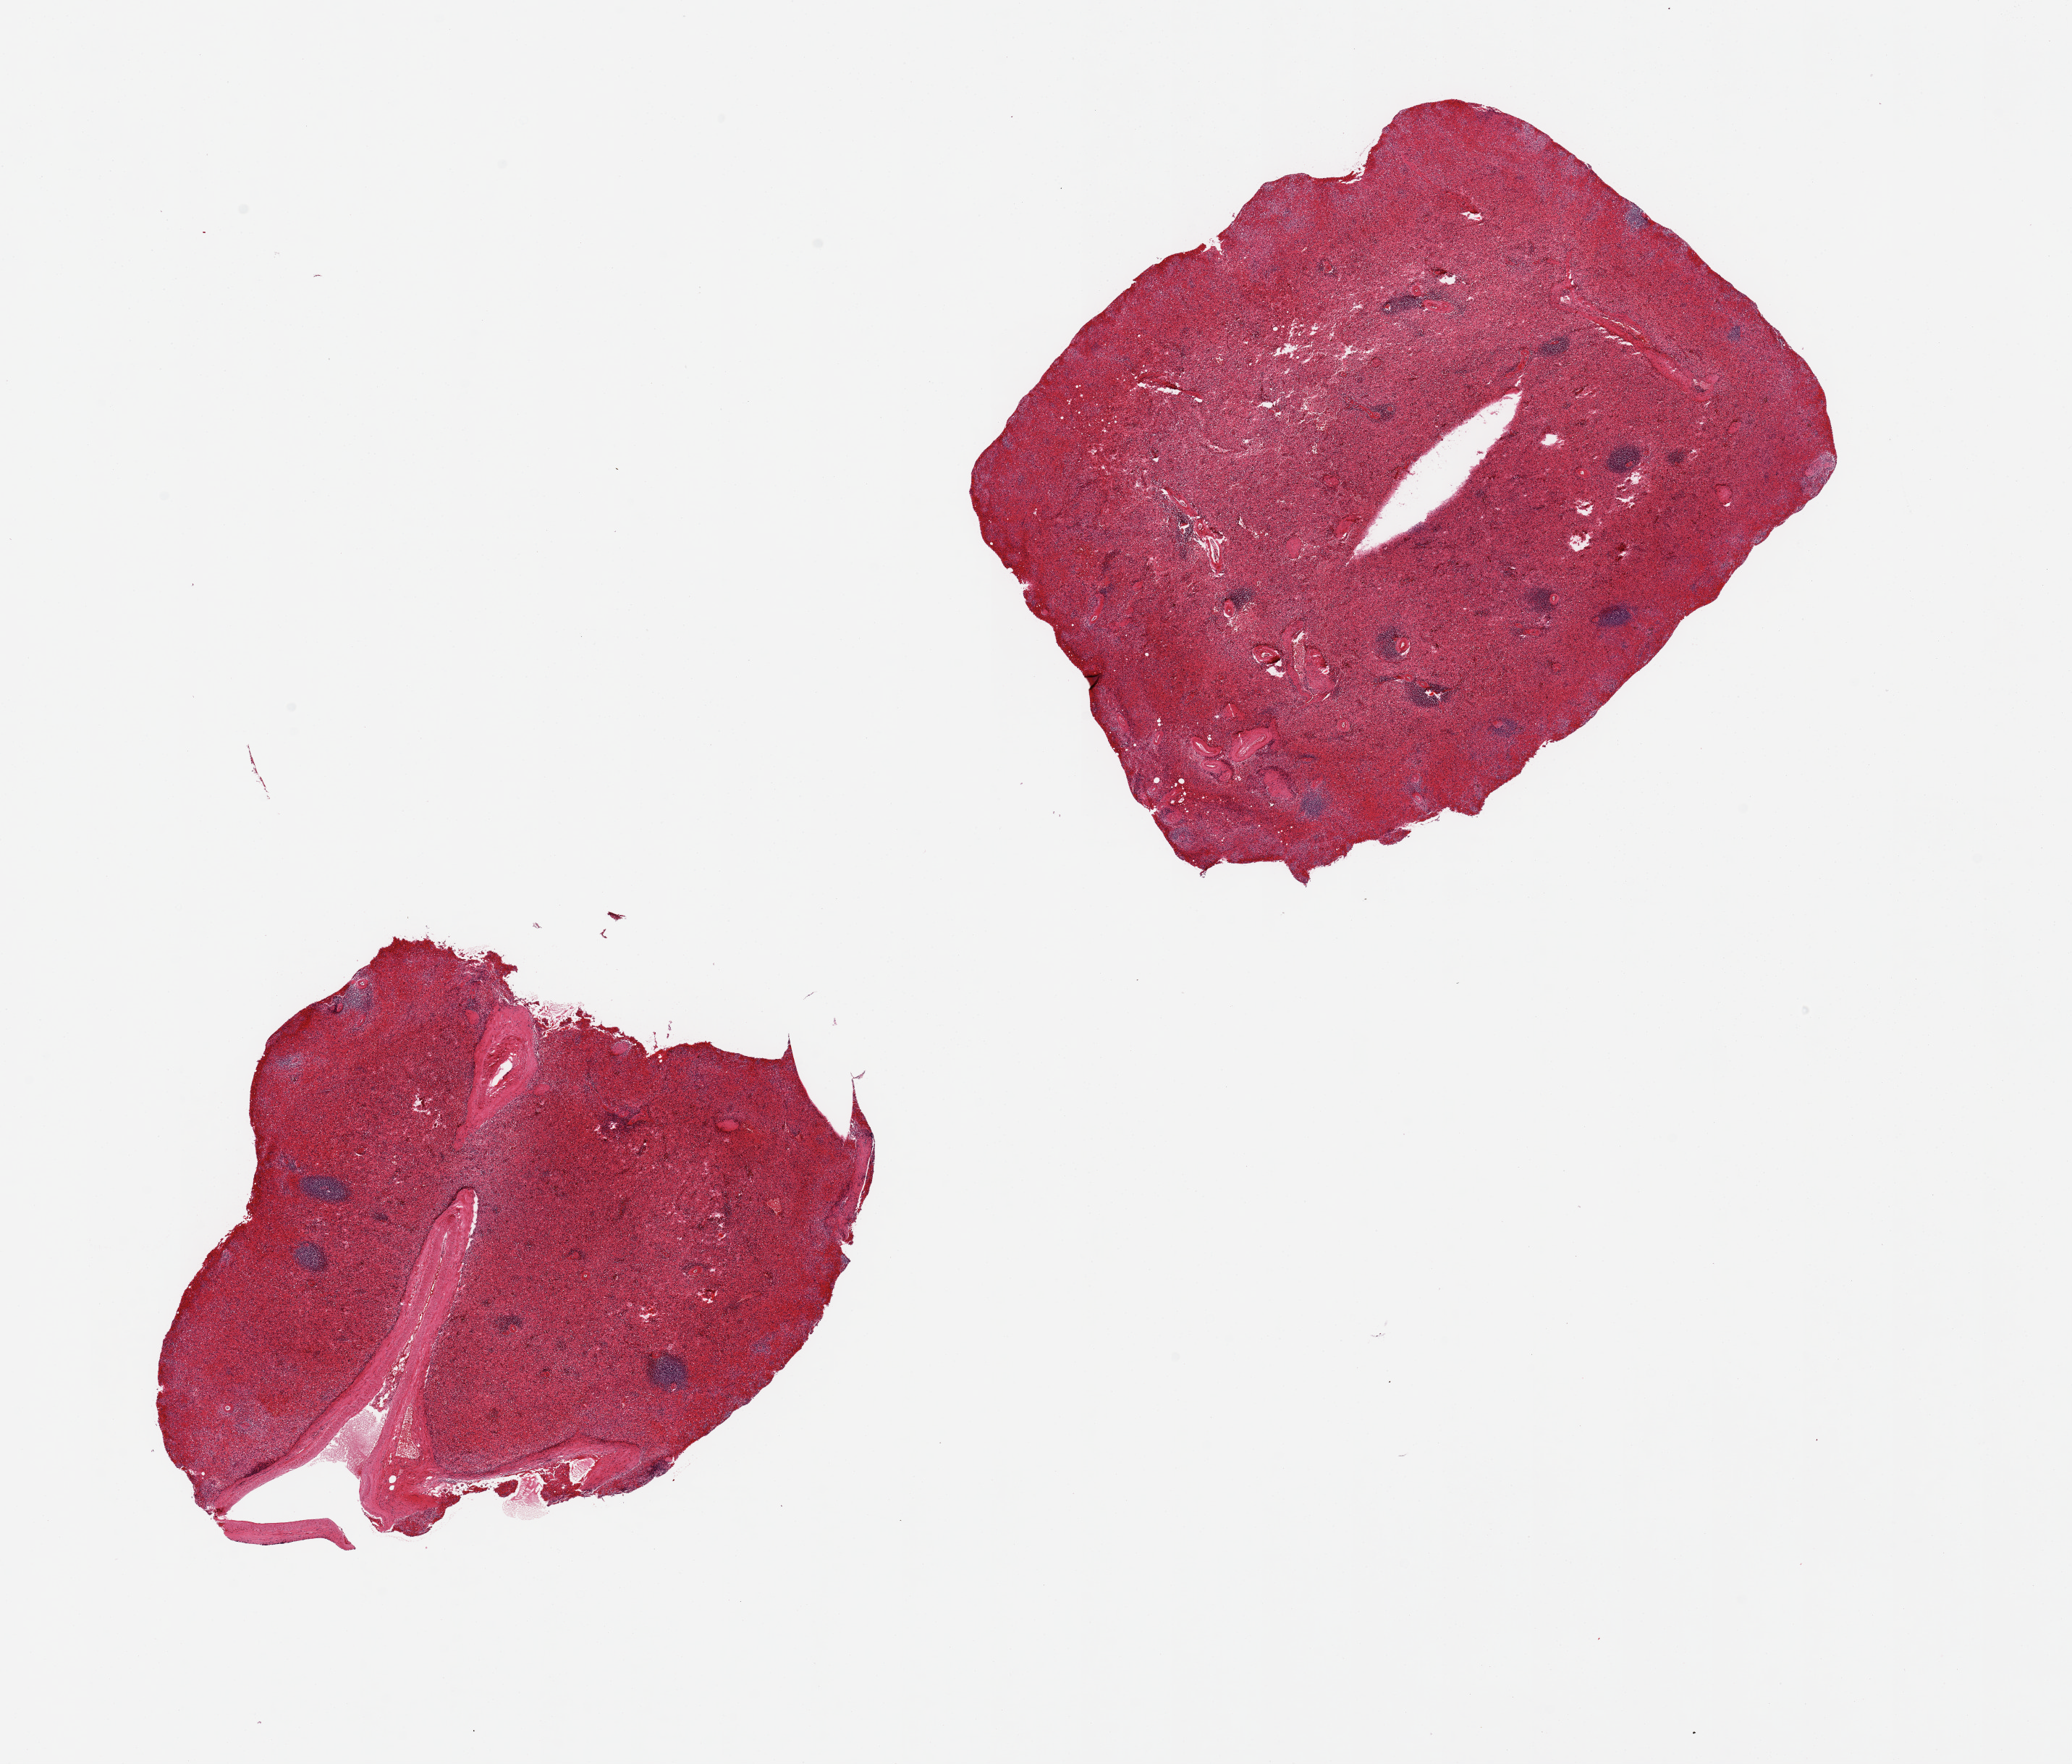
Digitized H&E-stained section, brightfield — whole scanned area (about 22.6 x 19.3 mm, from a 20x scan) shown as a low-resolution overview; PAXgene-fixed paraffin-embedded (PFPE) section; section of spleen (target tissue); tissue donor sample. Donor sex: male.
Reviewer comment on this tissue sample: 2 pieces, moderate congestion.